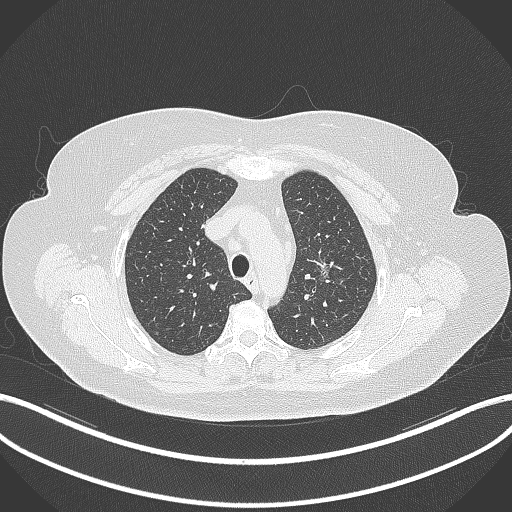
Chest CT, one axial slice. Slice 259 of 309 in the series (ordered by position). Reconstruction kernel B70f. Lung window (W 1500 / L -600 HU). 512 × 512 image matrix, field of view 400 × 400 mm. Female patient, age 70 years. From the clinical record (not read from this slice): clinical TNM (as recorded): T1c N0 M0.
Structures marked on this image (bounding box drawn by a radiologist):
- lung tumour (recorded histology: adenocarcinoma): bounding box (x1, y1, x2, y2) in pixels: (312, 252, 335, 287)